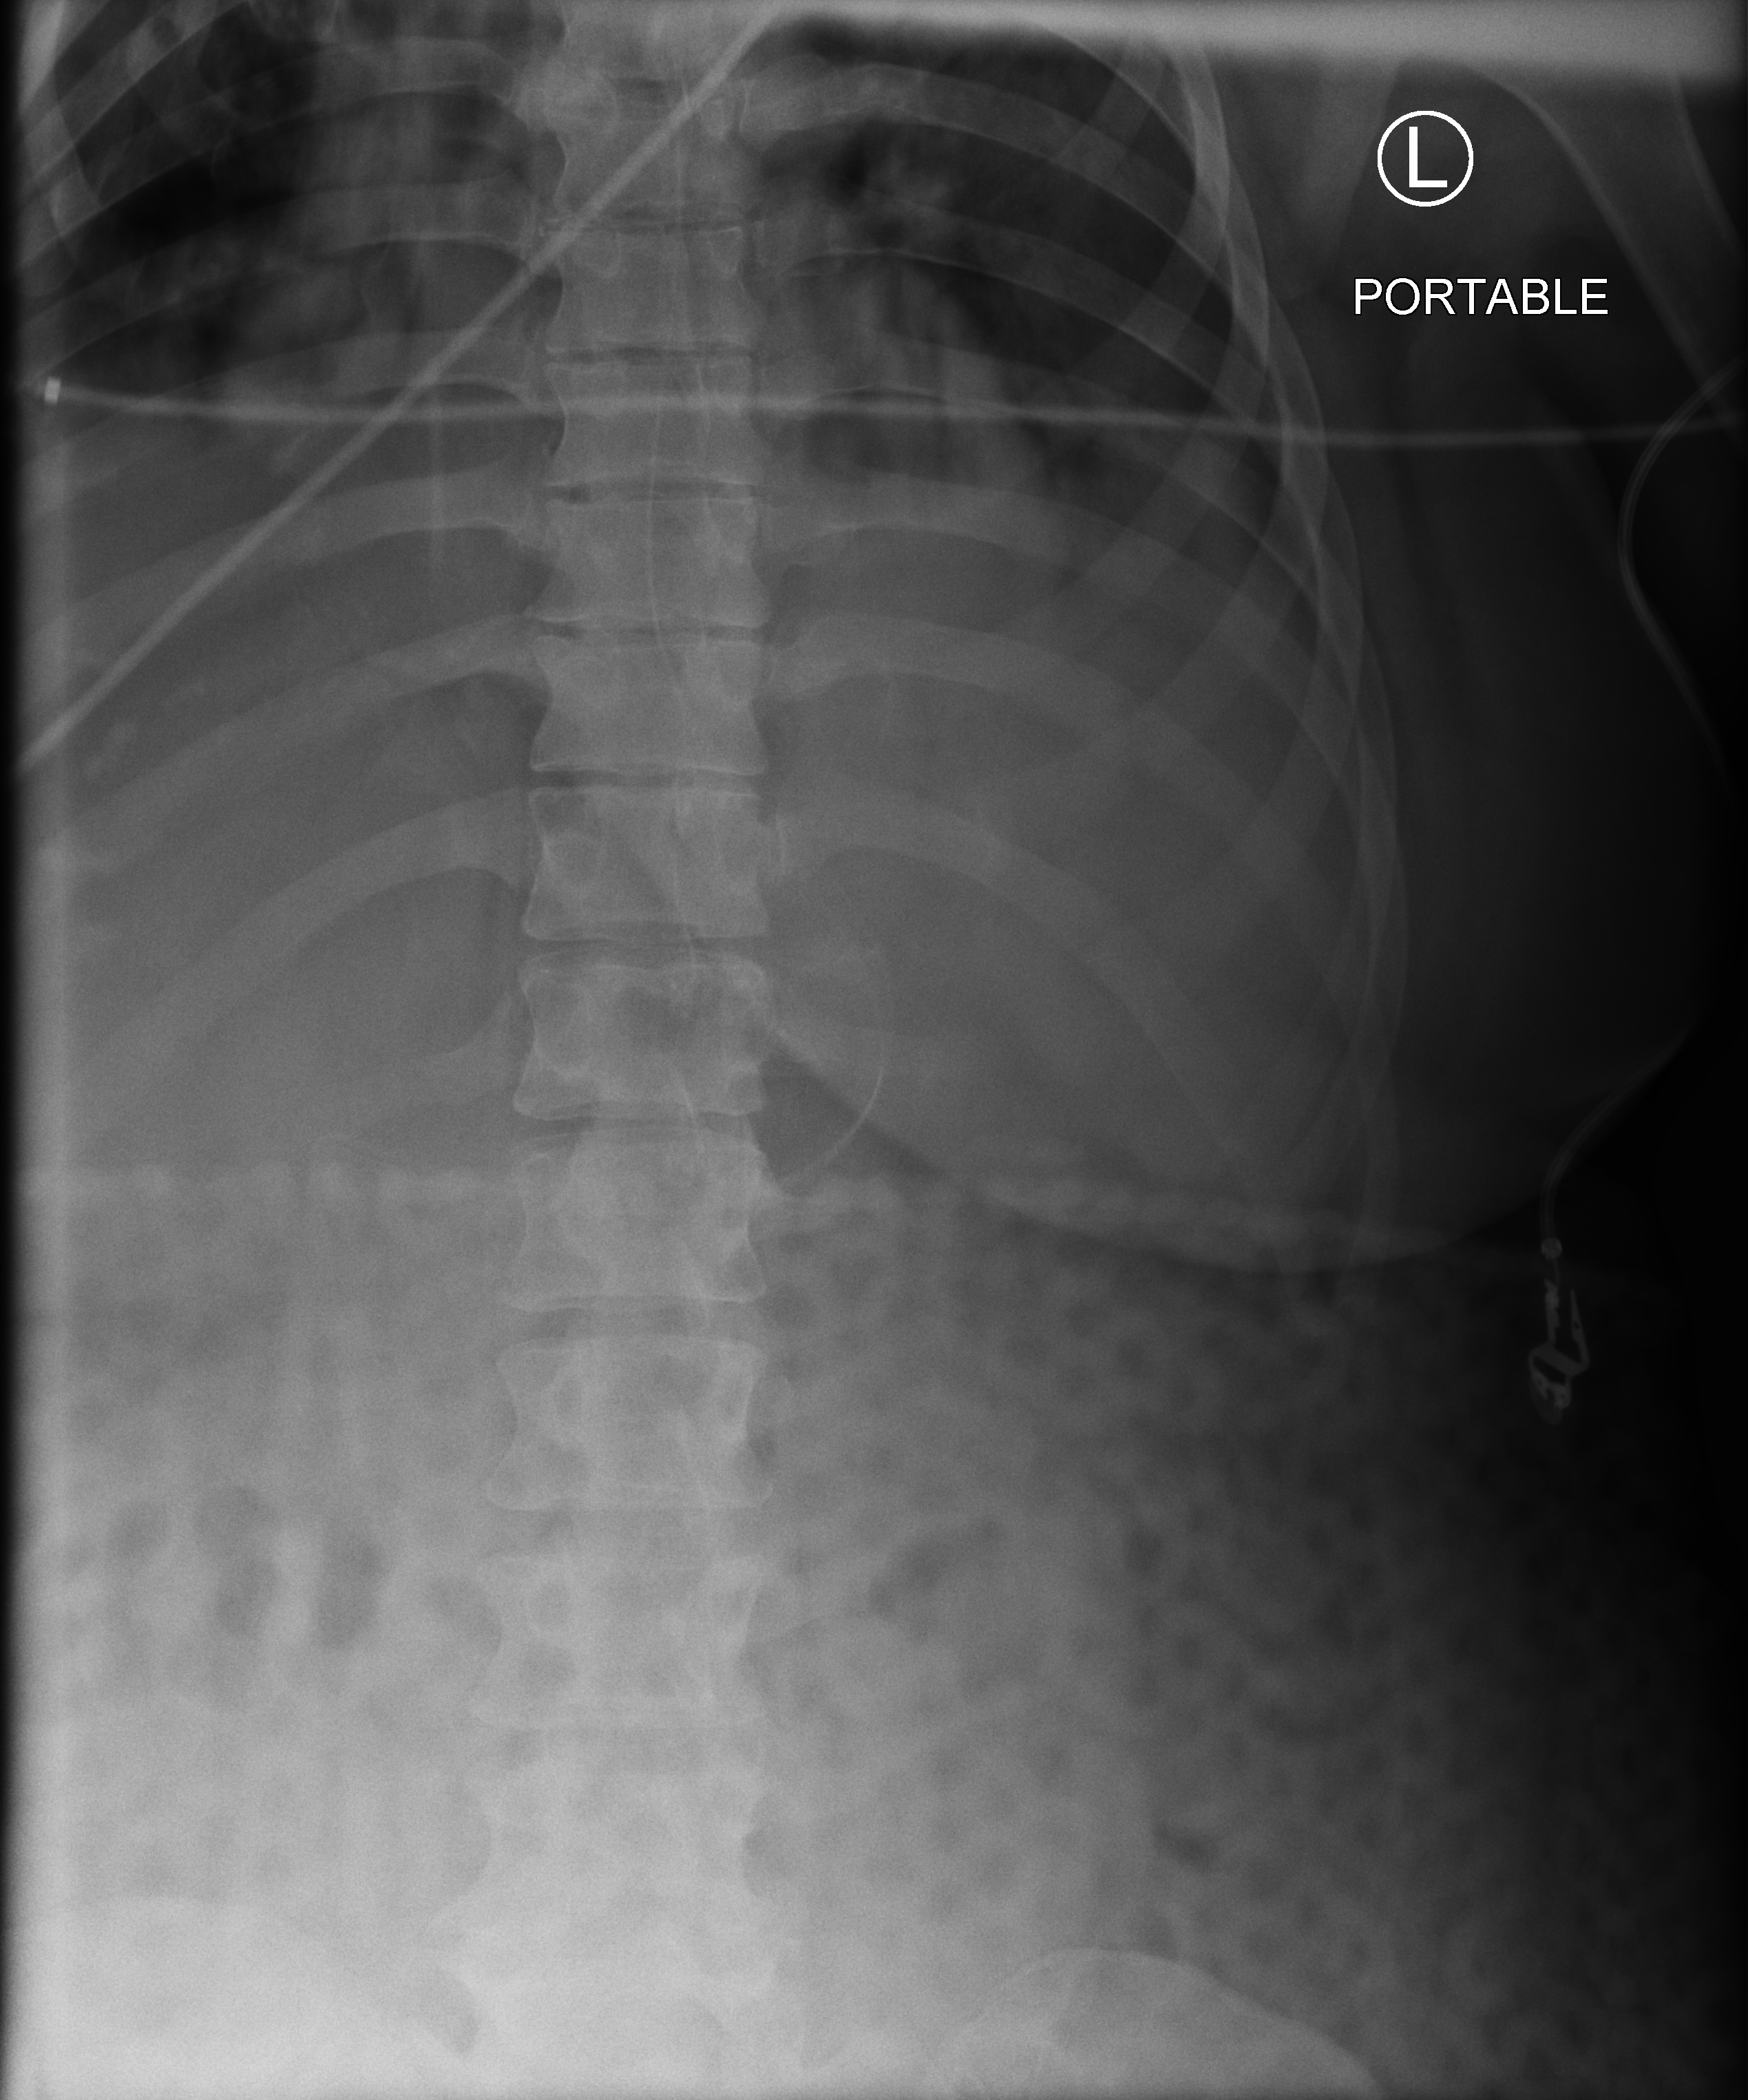
Abdomen X-ray (portable), anteroposterior (AP) projection. Patient hospitalised with COVID-19; female, aged 18–59 years.
From the hospital-stay record, not from the radiograph (when in the stay this image was taken is not recorded): length of hospital stay: 25 days.